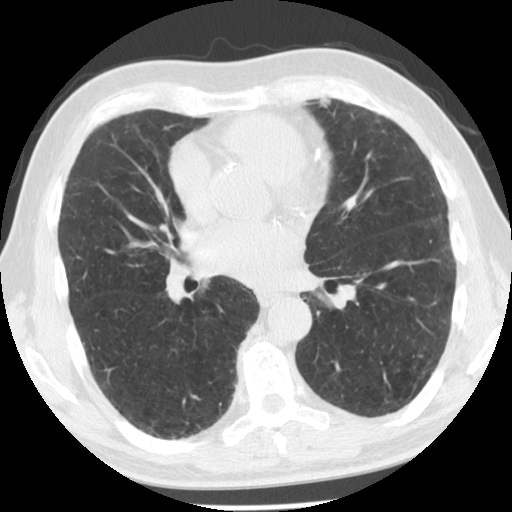
Low-dose screening chest CT, one axial slice. Position 62 of 129 along the scan axis. Reconstruction kernel STANDARD. 140 kVp. Lung window (W 1500 / L -600 HU). 2.5 mm slice thickness. 512 × 512 image matrix.
Outlined on this slice (manually delineated by an expert):
- lesion 1 (tumor, upper lobe of left lung): bounding box [x1, y1, x2, y2] px = [318, 97, 331, 108]